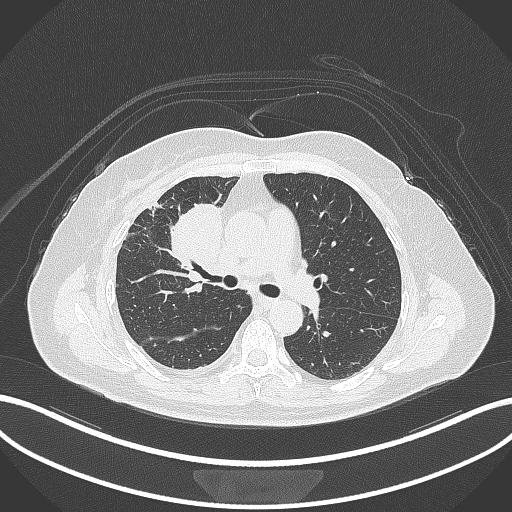
Chest CT, one axial slice; 120 kVp; lung window (W 1500 / L -600 HU); 512 × 512 image matrix, field of view 400 × 400 mm. Patient: female, 52 years. Case-level facts recorded for this patient, not image findings: clinical TNM (as recorded): T3 N1 M1.
Structures marked on this image (bounding box drawn by a radiologist):
- lung tumour (recorded histology: adenocarcinoma): bounding box [x1, y1, x2, y2] px = [166, 198, 223, 283]